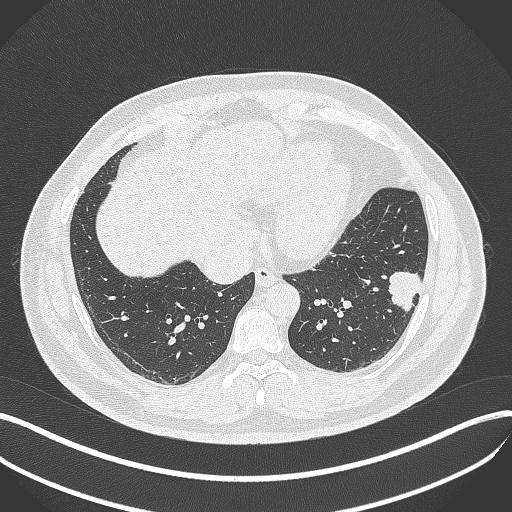
Chest CT, one axial slice. Slice 135 of 429 in the series (ordered by position). Reconstruction kernel B70f. Lung window (W 1500 / L -600 HU). 1 mm slice thickness. 512 × 512 image matrix, field of view 400 × 400 mm. Patient: male, 39 years. From the clinical record (not read from this slice): clinical TNM (as recorded): T2a N0 M0; histopathological grade: G2-3.
Structures marked on this image (rectangle marked by the reading radiologist):
- lung tumour (recorded histology: adenocarcinoma): bounding box [x1, y1, x2, y2] px = [385, 269, 424, 314]